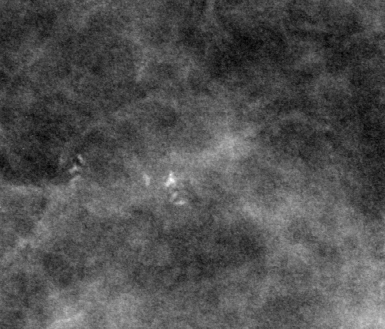
Cropped region of a digitized screen-film mammogram centred on a radiologist-marked abnormality; left breast; CC view; BI-RADS breast density category 2 (scale 1–4).
Calcifications, morphology pleomorphic, distribution clustered; BI-RADS assessment category 4; pathology (as recorded): benign.